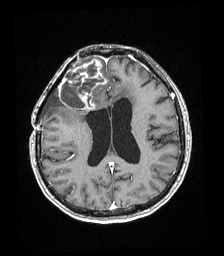
Brain MRI from a brain-tumour surgery series, one axial slice. Slice 83 of 192 in the series (ordered by position). T1-weighted post-contrast. 1 mm slice thickness. 224 × 256 image matrix, field of view 219 × 250 mm. Case-level facts recorded for this patient, not image findings: histopathology: Astrocytoma; WHO grade: 4; IDH mutation: yes; tumour location: Right superficial frontal.
Structures marked on this image (outlined manually by an expert reader):
- tumour: bounding box <59,59,106,110> (left, top, right, bottom; pixels)